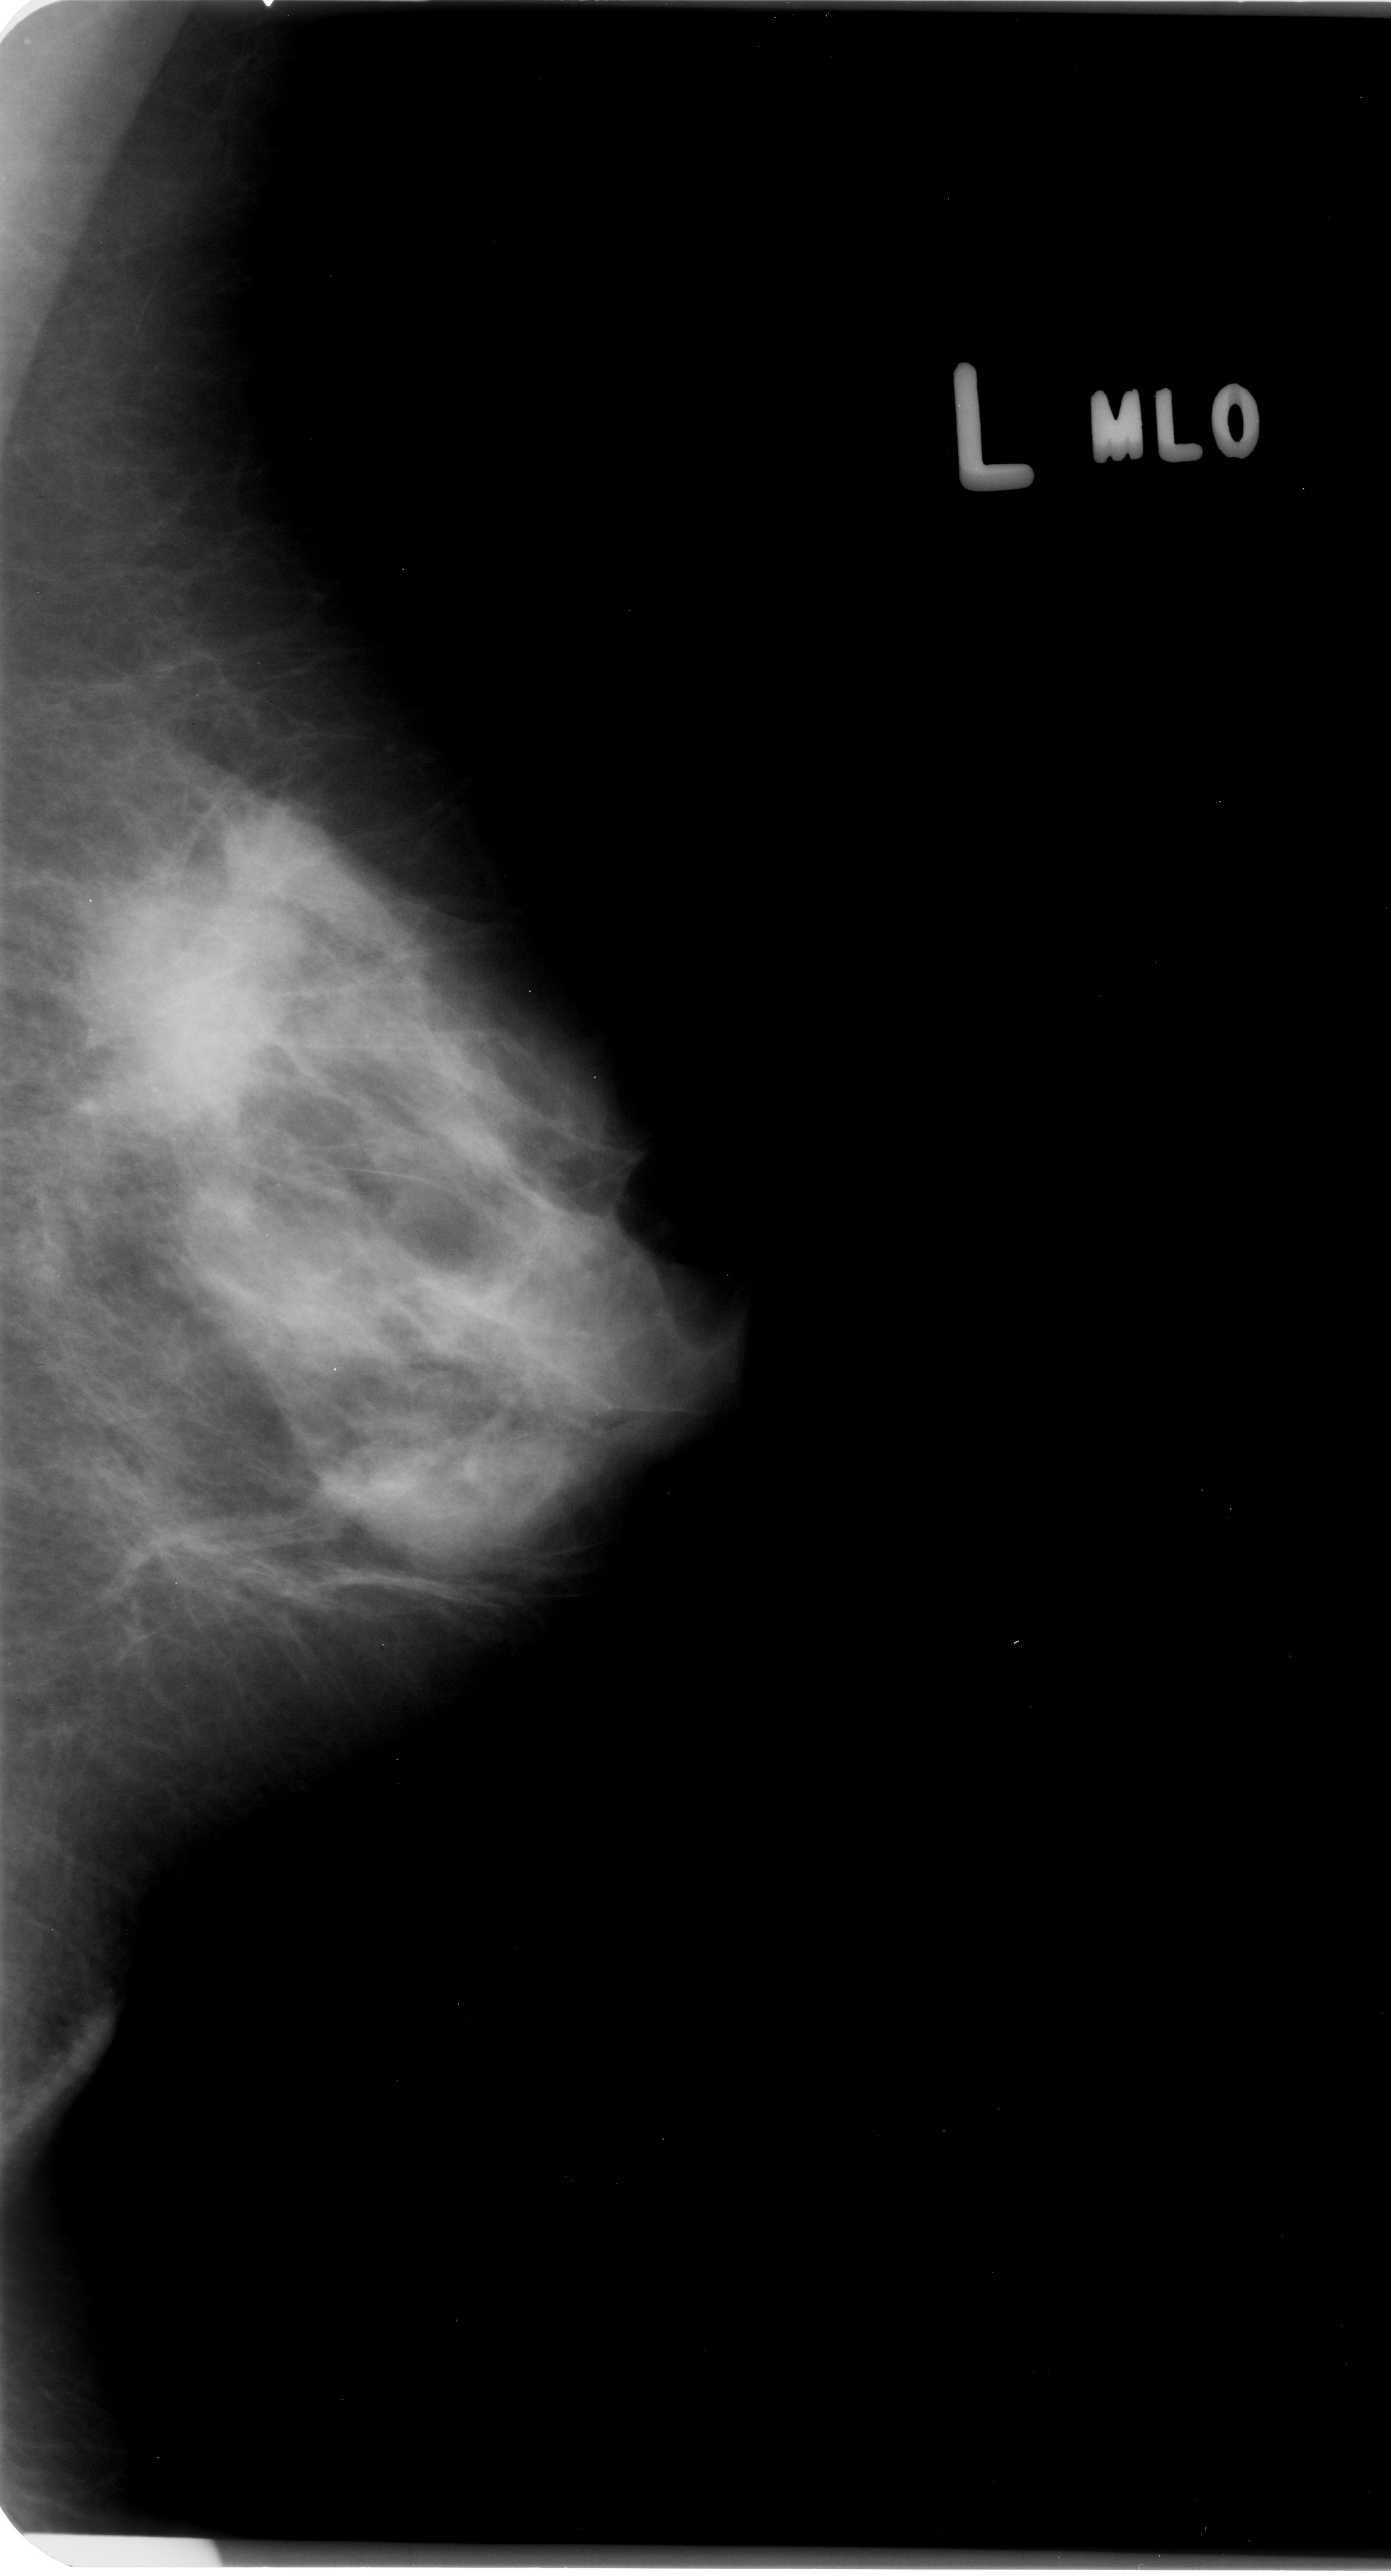
Digitized screen-film mammogram, left breast, MLO view, BI-RADS breast density category 3 (scale 1–4).
Marked findings (only marked abnormalities are described; nothing is implied about the rest of the image): mass, shape irregular / architectural distortion, margins obscured / spiculated; BI-RADS assessment category 4; pathology result (as recorded, not read from the image): malignant.